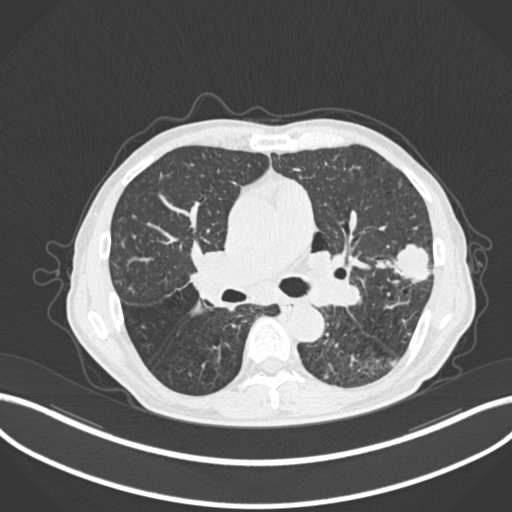
Chest CT, one axial slice; slice 140 of 287 in the series (ordered by position); lung window (W 1500 / L -600 HU); 1 mm slice thickness; 512 × 512 image matrix, field of view 400 × 400 mm. Patient: male, 74 years. From the clinical record (not read from this slice): clinical TNM (as recorded): T2a N1 M0.
Annotated regions visible in this slice (bounding box drawn by a radiologist):
- lung tumour (recorded histology: adenocarcinoma): bounding box [x1, y1, x2, y2] px = [378, 243, 432, 286]